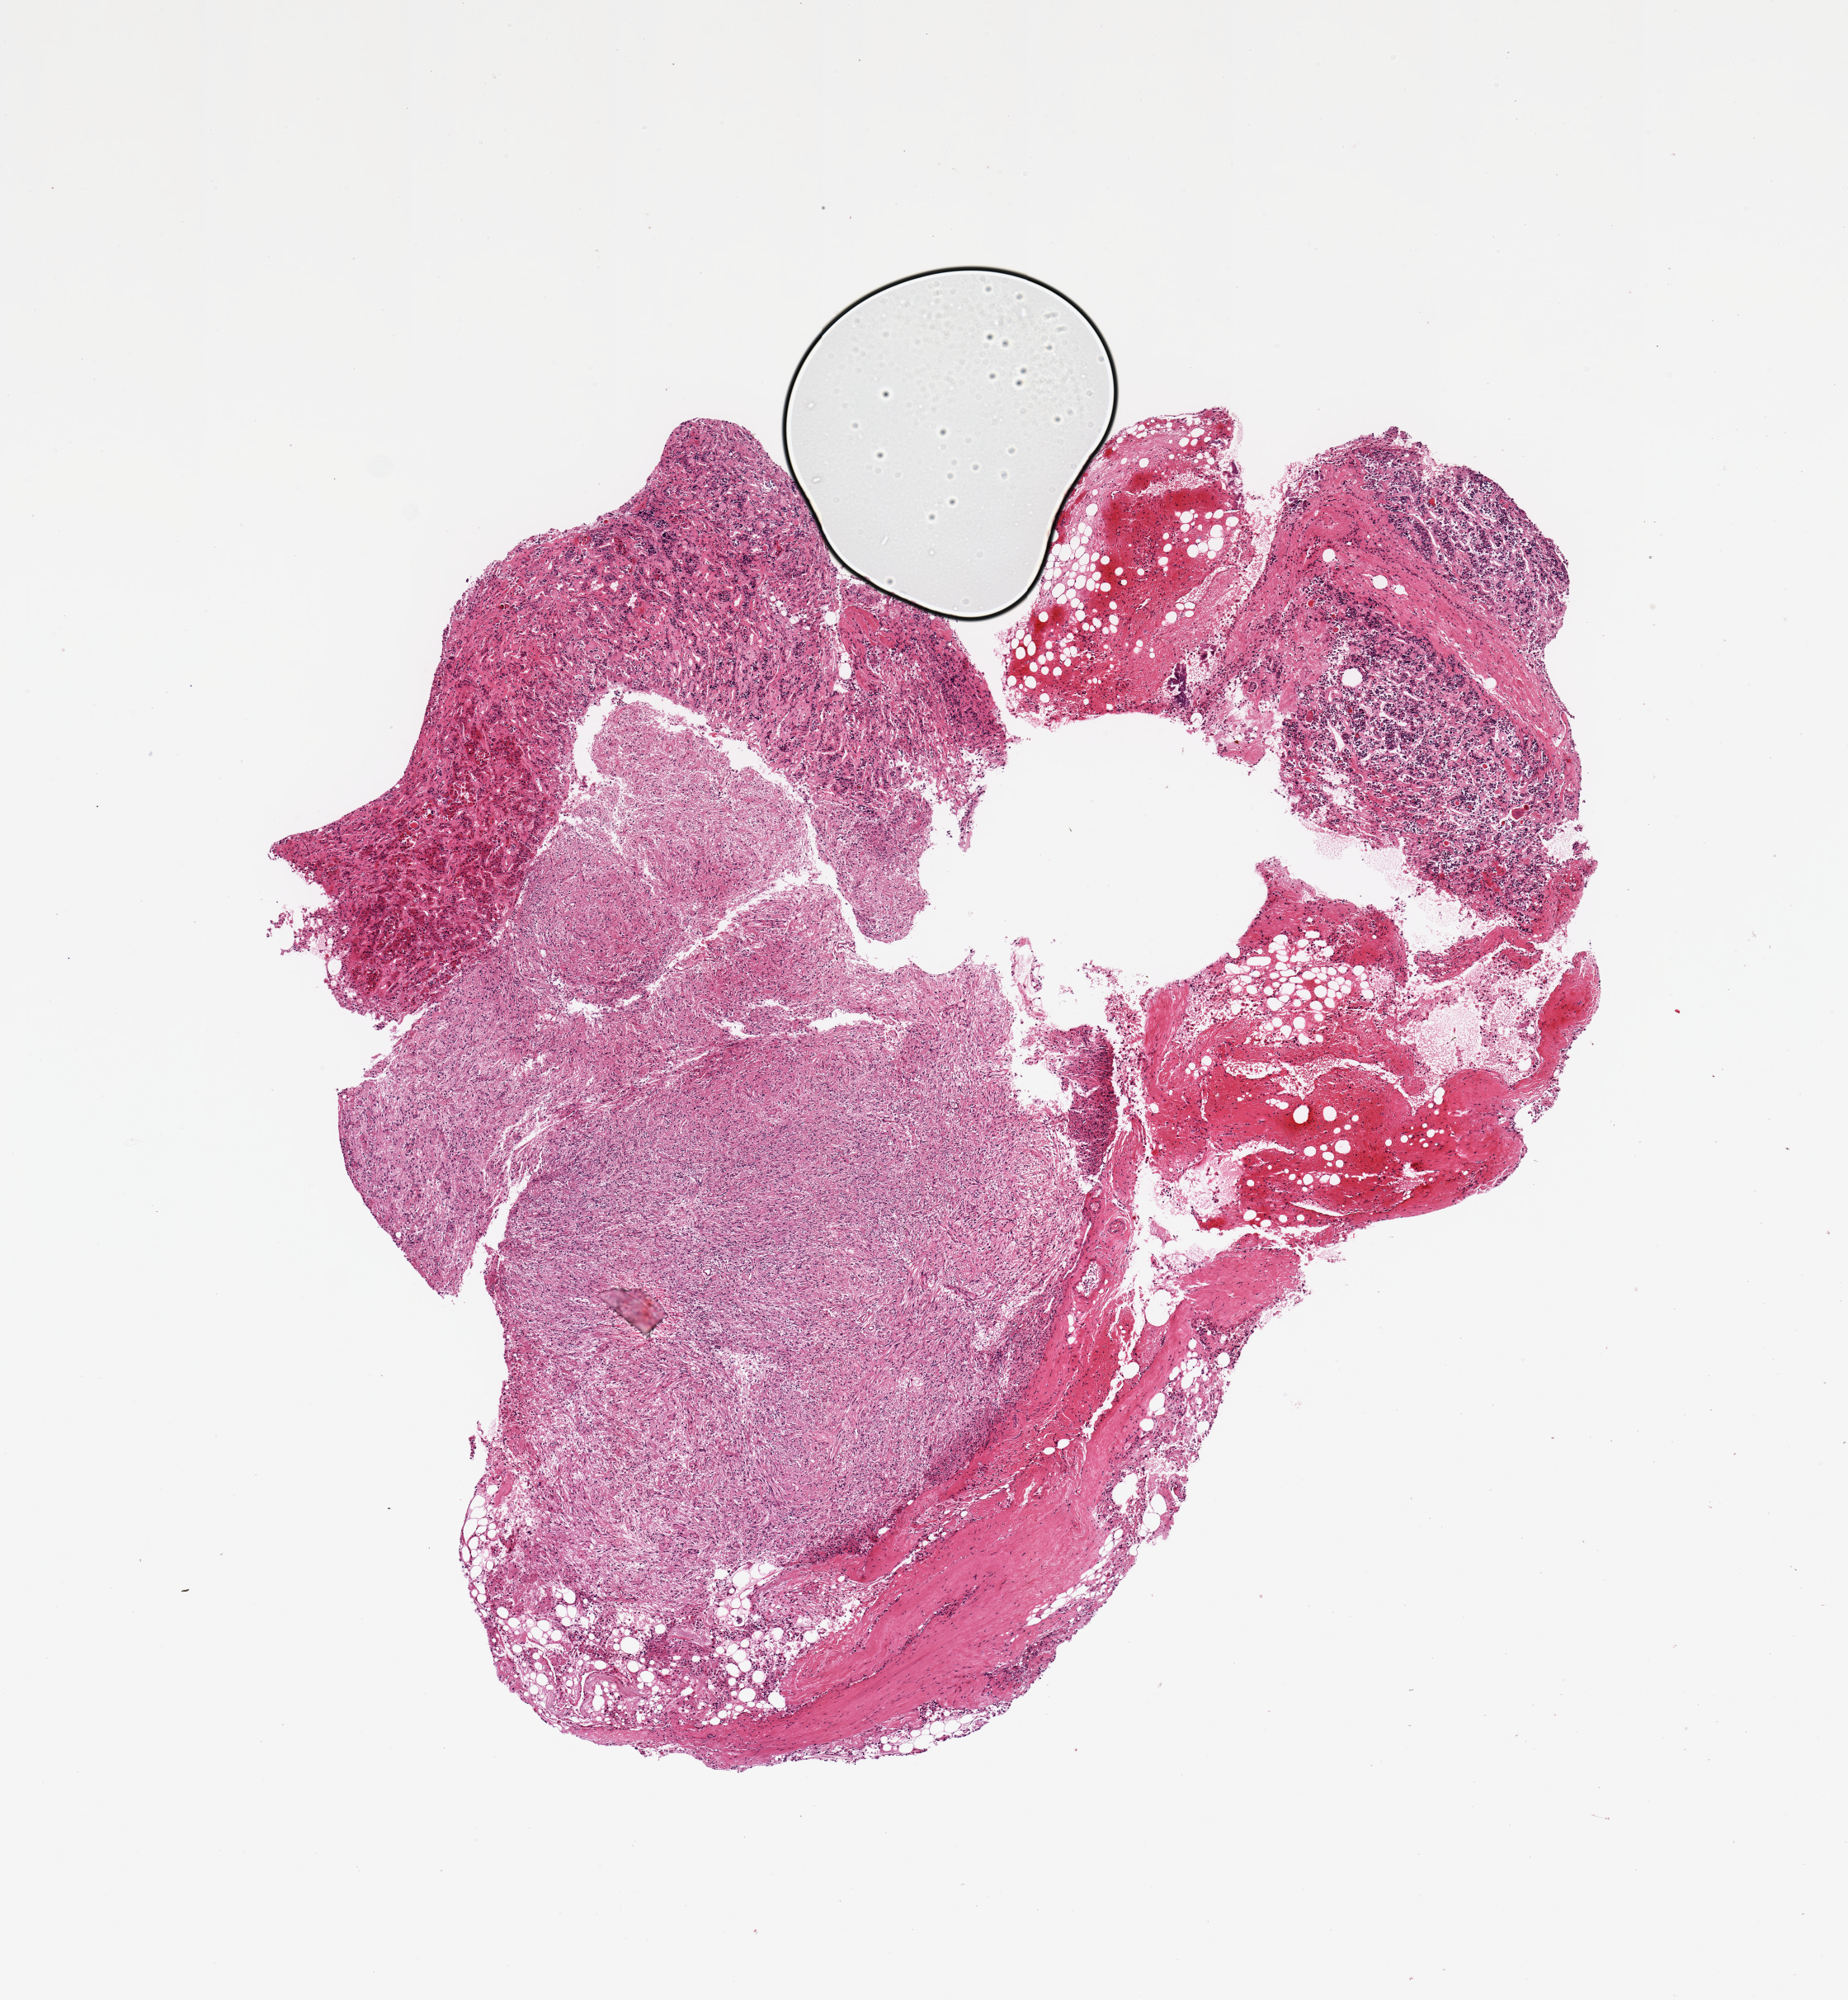
Whole-slide image, haematoxylin and eosin stain, a low-resolution overview of the entire scanned area, about 8.9 x 9.6 mm (acquisition: 20x scan). PAXgene-fixed, paraffin-embedded tissue. Section of pituitary (target tissue). Tissue donor sample. Donor sex: male.
* reviewer comment on this tissue sample: 1 piece; mainly neurohypophysis, ~4.5mm--smaller nubbins of adenohypophysis